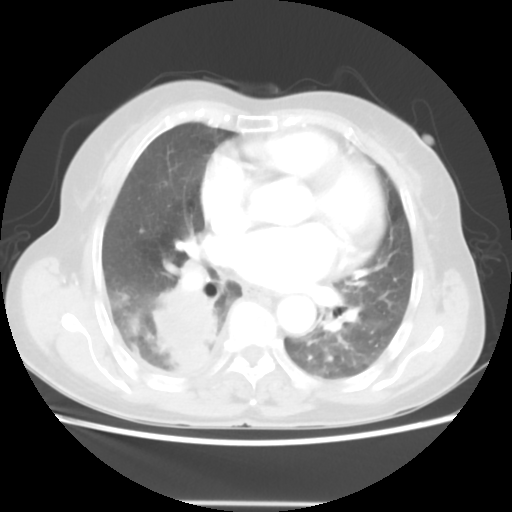
Chest CT, one axial slice; slice 25 of 52 in the series (ordered by position); reconstruction kernel STANDARD; 140 kVp; lung window (W 1500 / L -600 HU); 5 mm slice thickness; 512 × 512 image matrix, field of view 337 × 337 mm. Patient: female, 67 years. Case-level facts recorded for this patient, not image findings: clinical TNM (as recorded): T3 N1 M1.
Structures marked on this image (rectangle marked by the reading radiologist):
- lung tumour (recorded histology: adenocarcinoma): bounding box <138,267,223,385> (left, top, right, bottom; pixels)